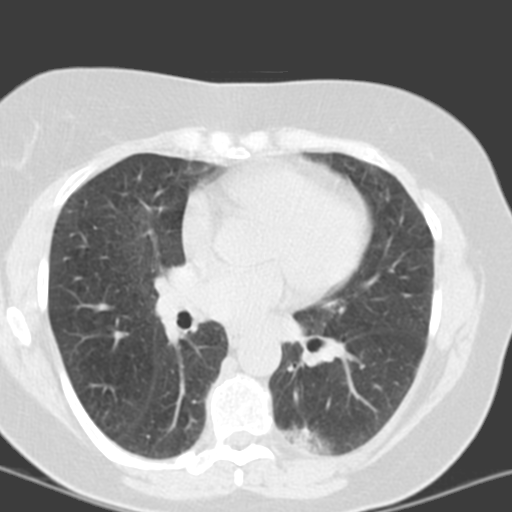
Low-dose screening chest CT, one axial slice; position 82 of 150 along the scan axis; 120 kVp; lung window (W 1500 / L -600 HU); 3.2 mm slice thickness; 512 × 512 image matrix, field of view 290 × 290 mm.
Structures marked on this image (expert manual segmentation):
- lesion 2 (tumor, lower lobe of left lung): bounding box (x1, y1, x2, y2) in pixels: (292, 431, 314, 453)